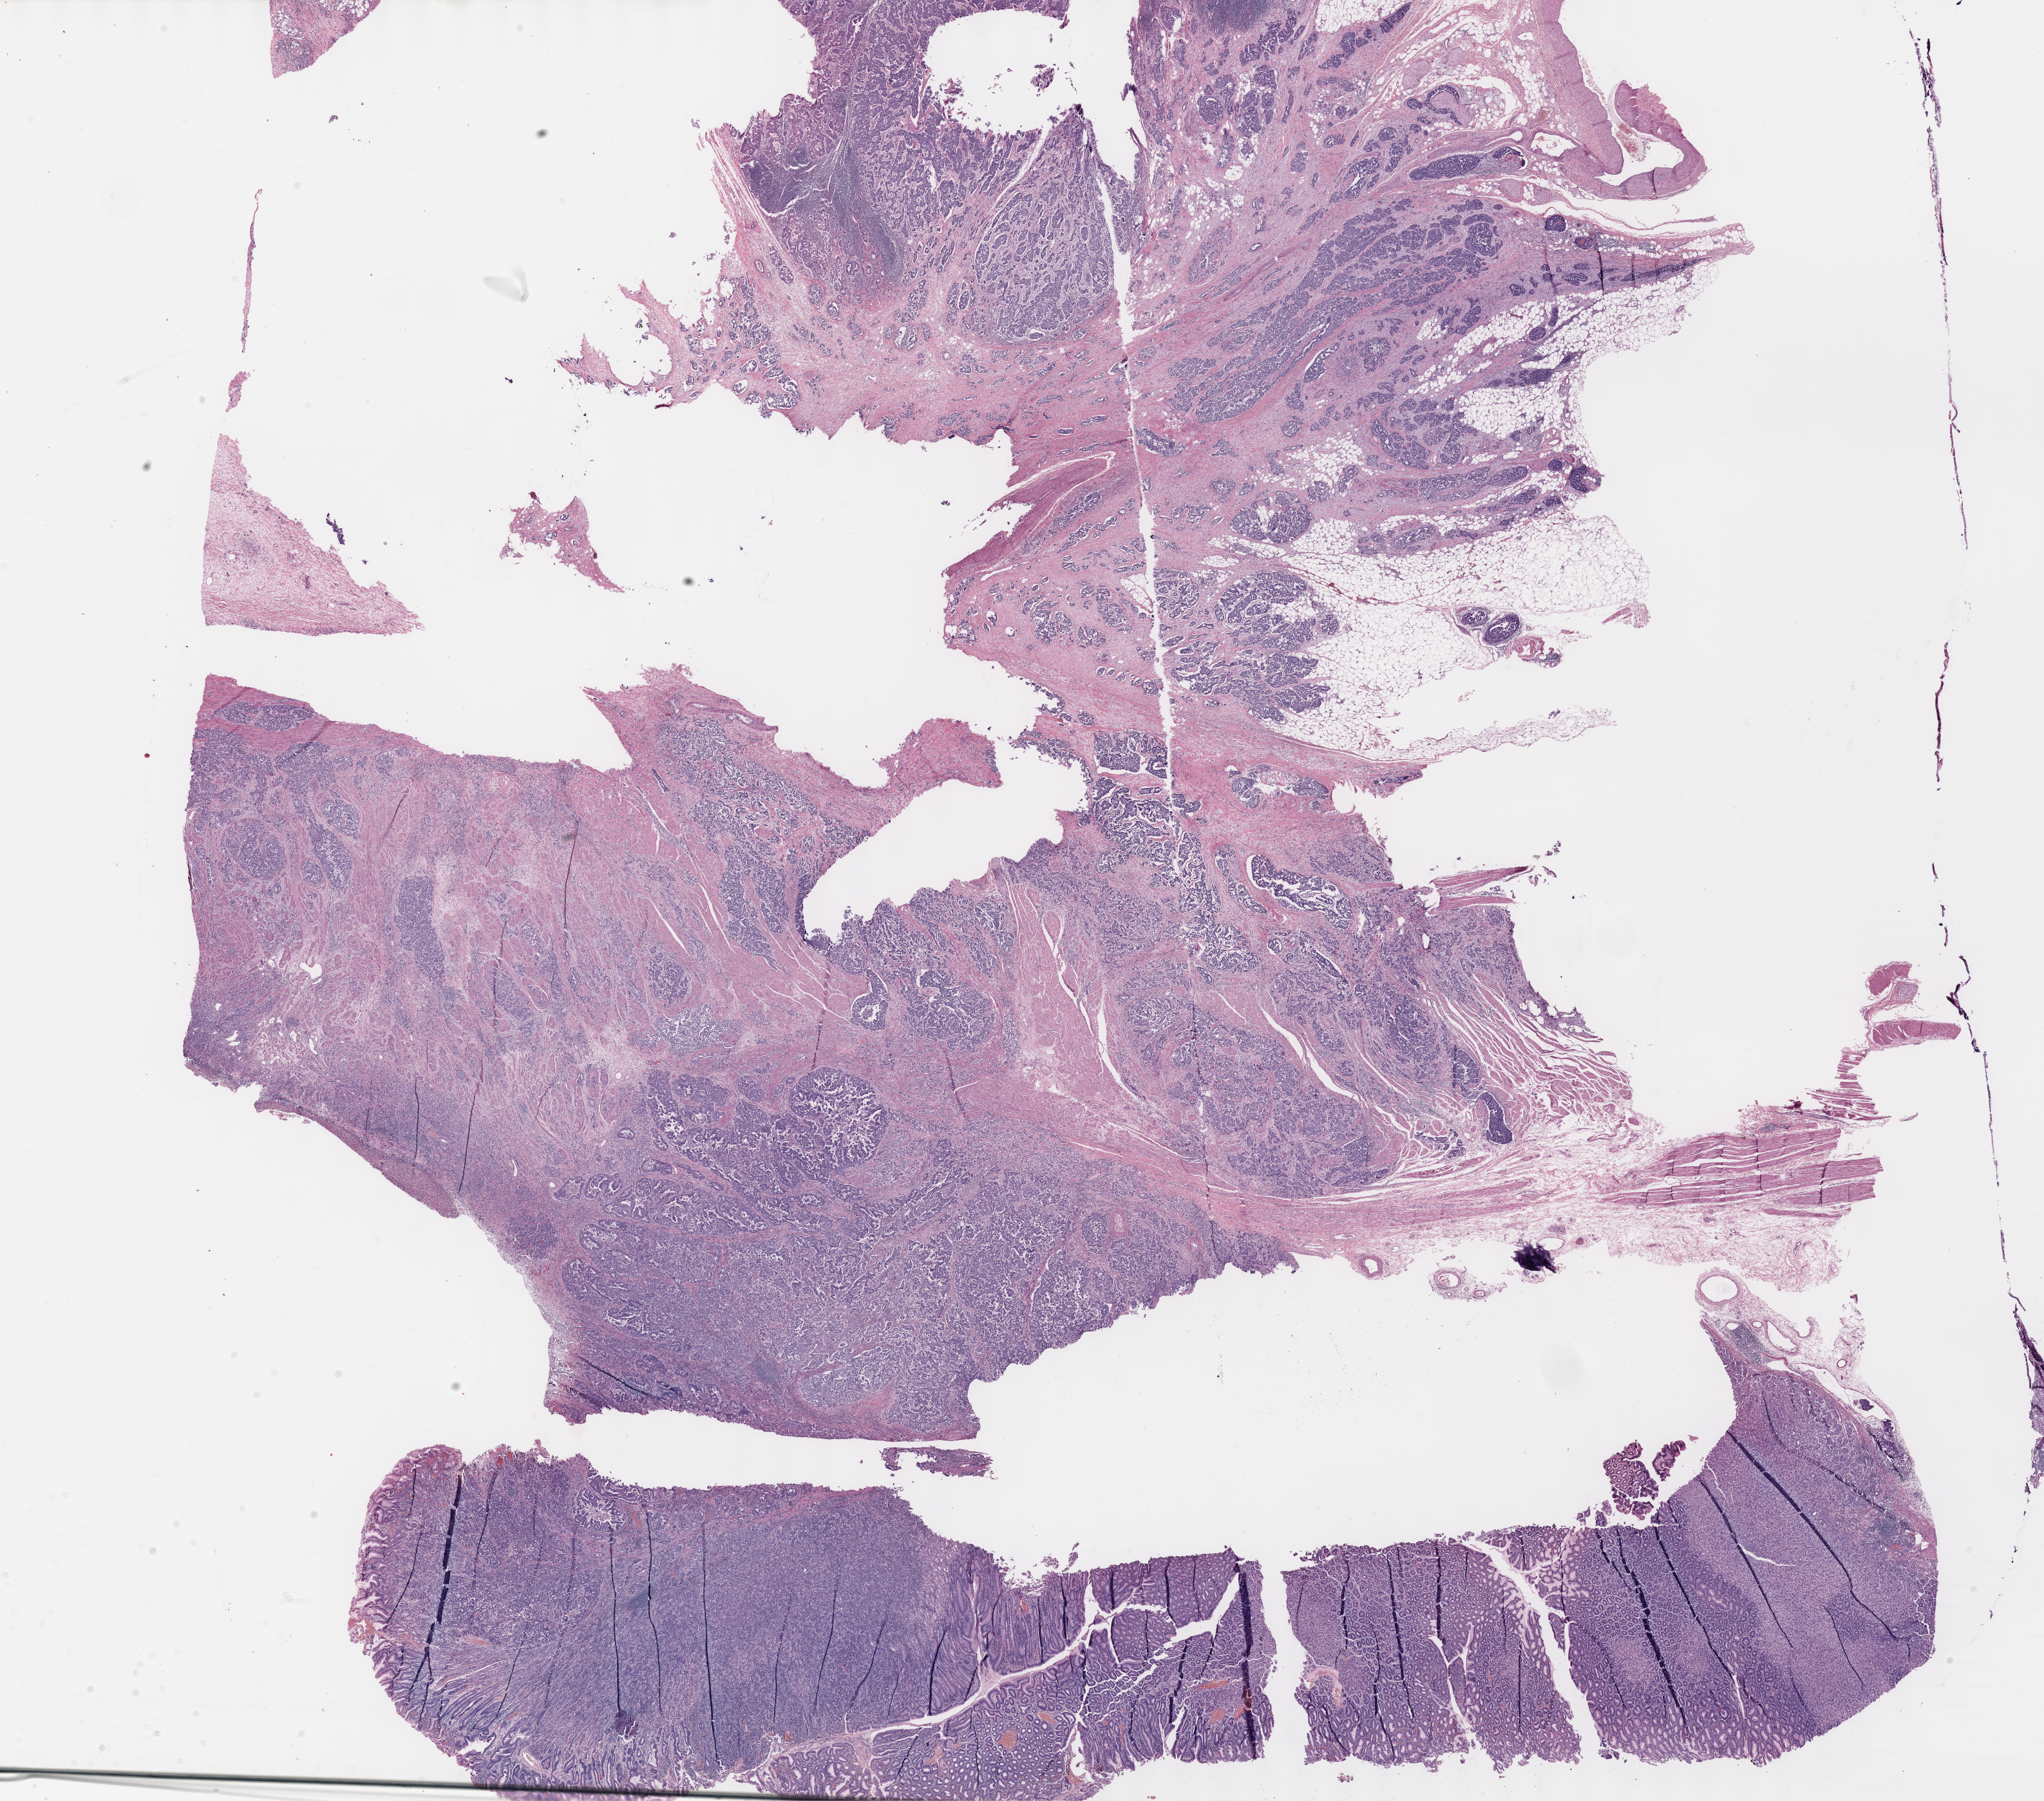
Whole-slide histology image, H&E-stained — a low-resolution overview of the entire scanned area, about 25.7 x 22.6 mm, formalin-fixed paraffin-embedded (FFPE) diagnostic section, stomach, primary tumour sample. Male patient; age at initial diagnosis 68 years. Histologic grade: G3 (poorly differentiated).
AJCC pathologic stage: IIIB. TNM: T3 N3 M0. Histologic diagnosis: Adenocarcinoma, NOS (cardia, NOS).